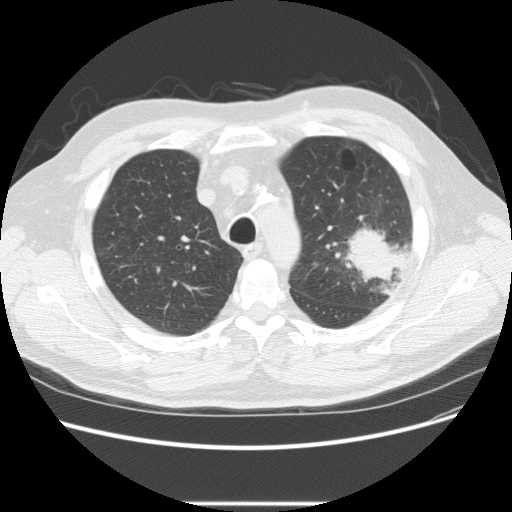
Low-dose screening chest CT, one axial slice. Slice 175 of 233 in the series (ordered by position). Reconstruction kernel STANDARD. 120 kVp. Lung window (W 1500 / L -600 HU). 2.5 mm slice thickness. 512 × 512 image matrix.
Outlined on this slice (manually delineated by an expert):
- lesion 1 (tumor, upper lobe of left lung): bounding box <345,226,401,286> (left, top, right, bottom; pixels)